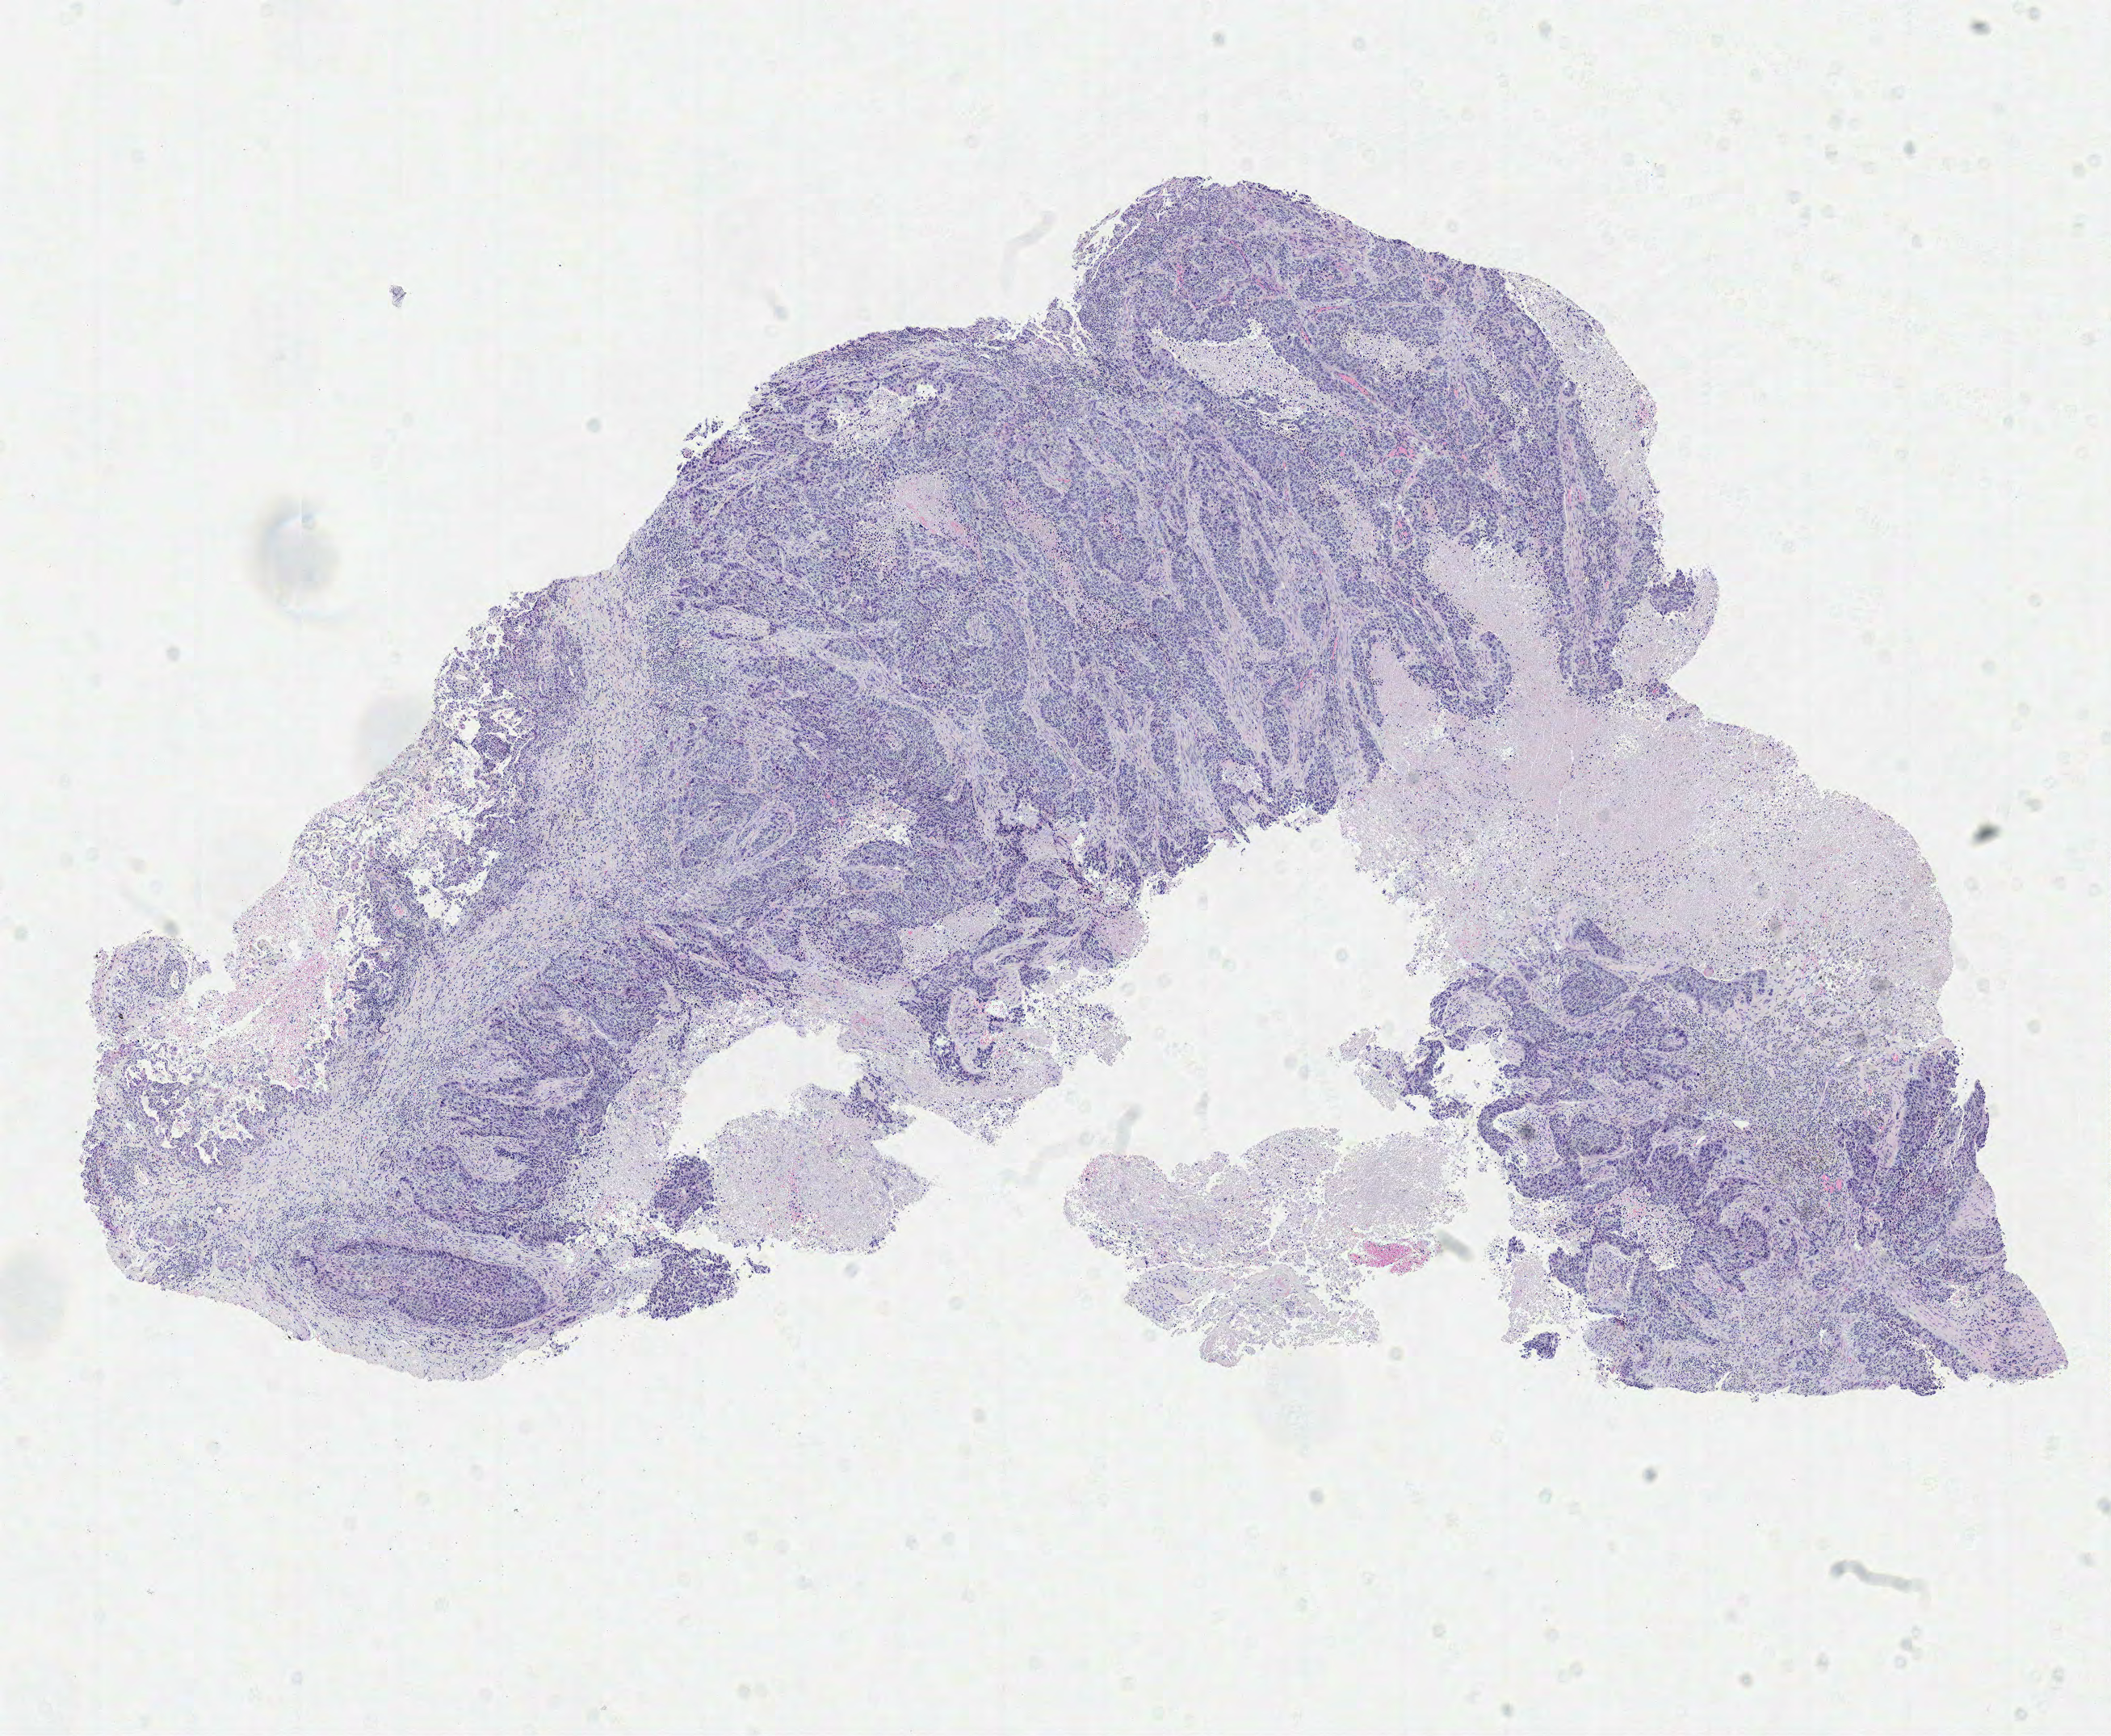
Digitized H&E tissue section (whole slide) — low-resolution overview of the scanned area, about 10.3 x 8.5 mm (from a 40x scan), formalin-fixed paraffin-embedded (FFPE) diagnostic section, sample: primary tumour, lung. Male, age 58 years at initial diagnosis.
Laterality: left. Pathologic diagnosis: Squamous cell carcinoma, NOS (lower lobe, lung). AJCC pathologic stage: IIB (6th edition).